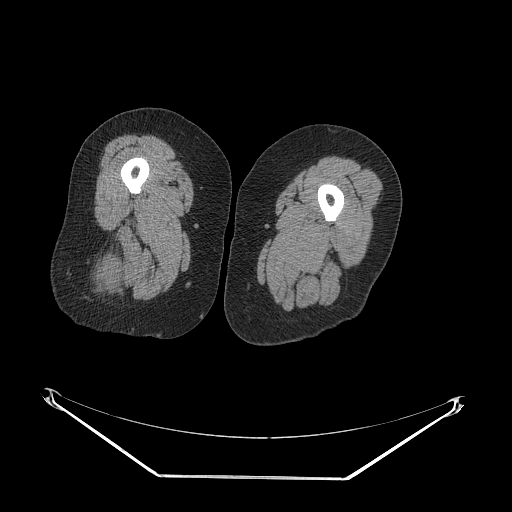
CT of an extremity soft-tissue mass (from a PET/CT study), one axial slice; position 25 of 257 along the scan axis; soft-tissue window (W 400 / L 40 HU); 3.75 mm slice thickness; 512 × 512 image matrix. Female patient. Case-level facts recorded for this patient, not image findings: histological type: synovial sarcoma; grade: intermediate; site of the primary tumour: right buttock.
Structures marked on this image (expert contour drawn on MRI and transferred to this co-registered scan by the dataset authors):
- gross tumour volume including surrounding oedema: bounding box (x1, y1, x2, y2) in pixels: (94, 242, 122, 291)